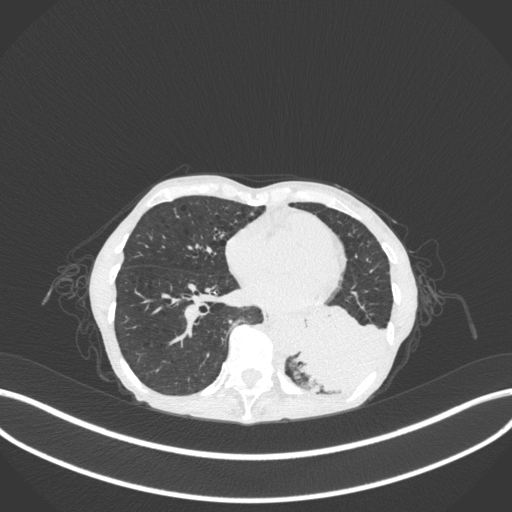
Chest CT, one axial slice. Lung window (W 1500 / L -600 HU). 512 × 512 image matrix, field of view 400 × 400 mm. Patient: female, 70 years. Case-level facts recorded for this patient, not image findings: clinical TNM (as recorded): T3 N0 M0.
Annotated regions visible in this slice (bounding box drawn by a radiologist):
- lung tumour (recorded histology: small cell carcinoma): bounding box [x1, y1, x2, y2] px = [290, 300, 396, 398]